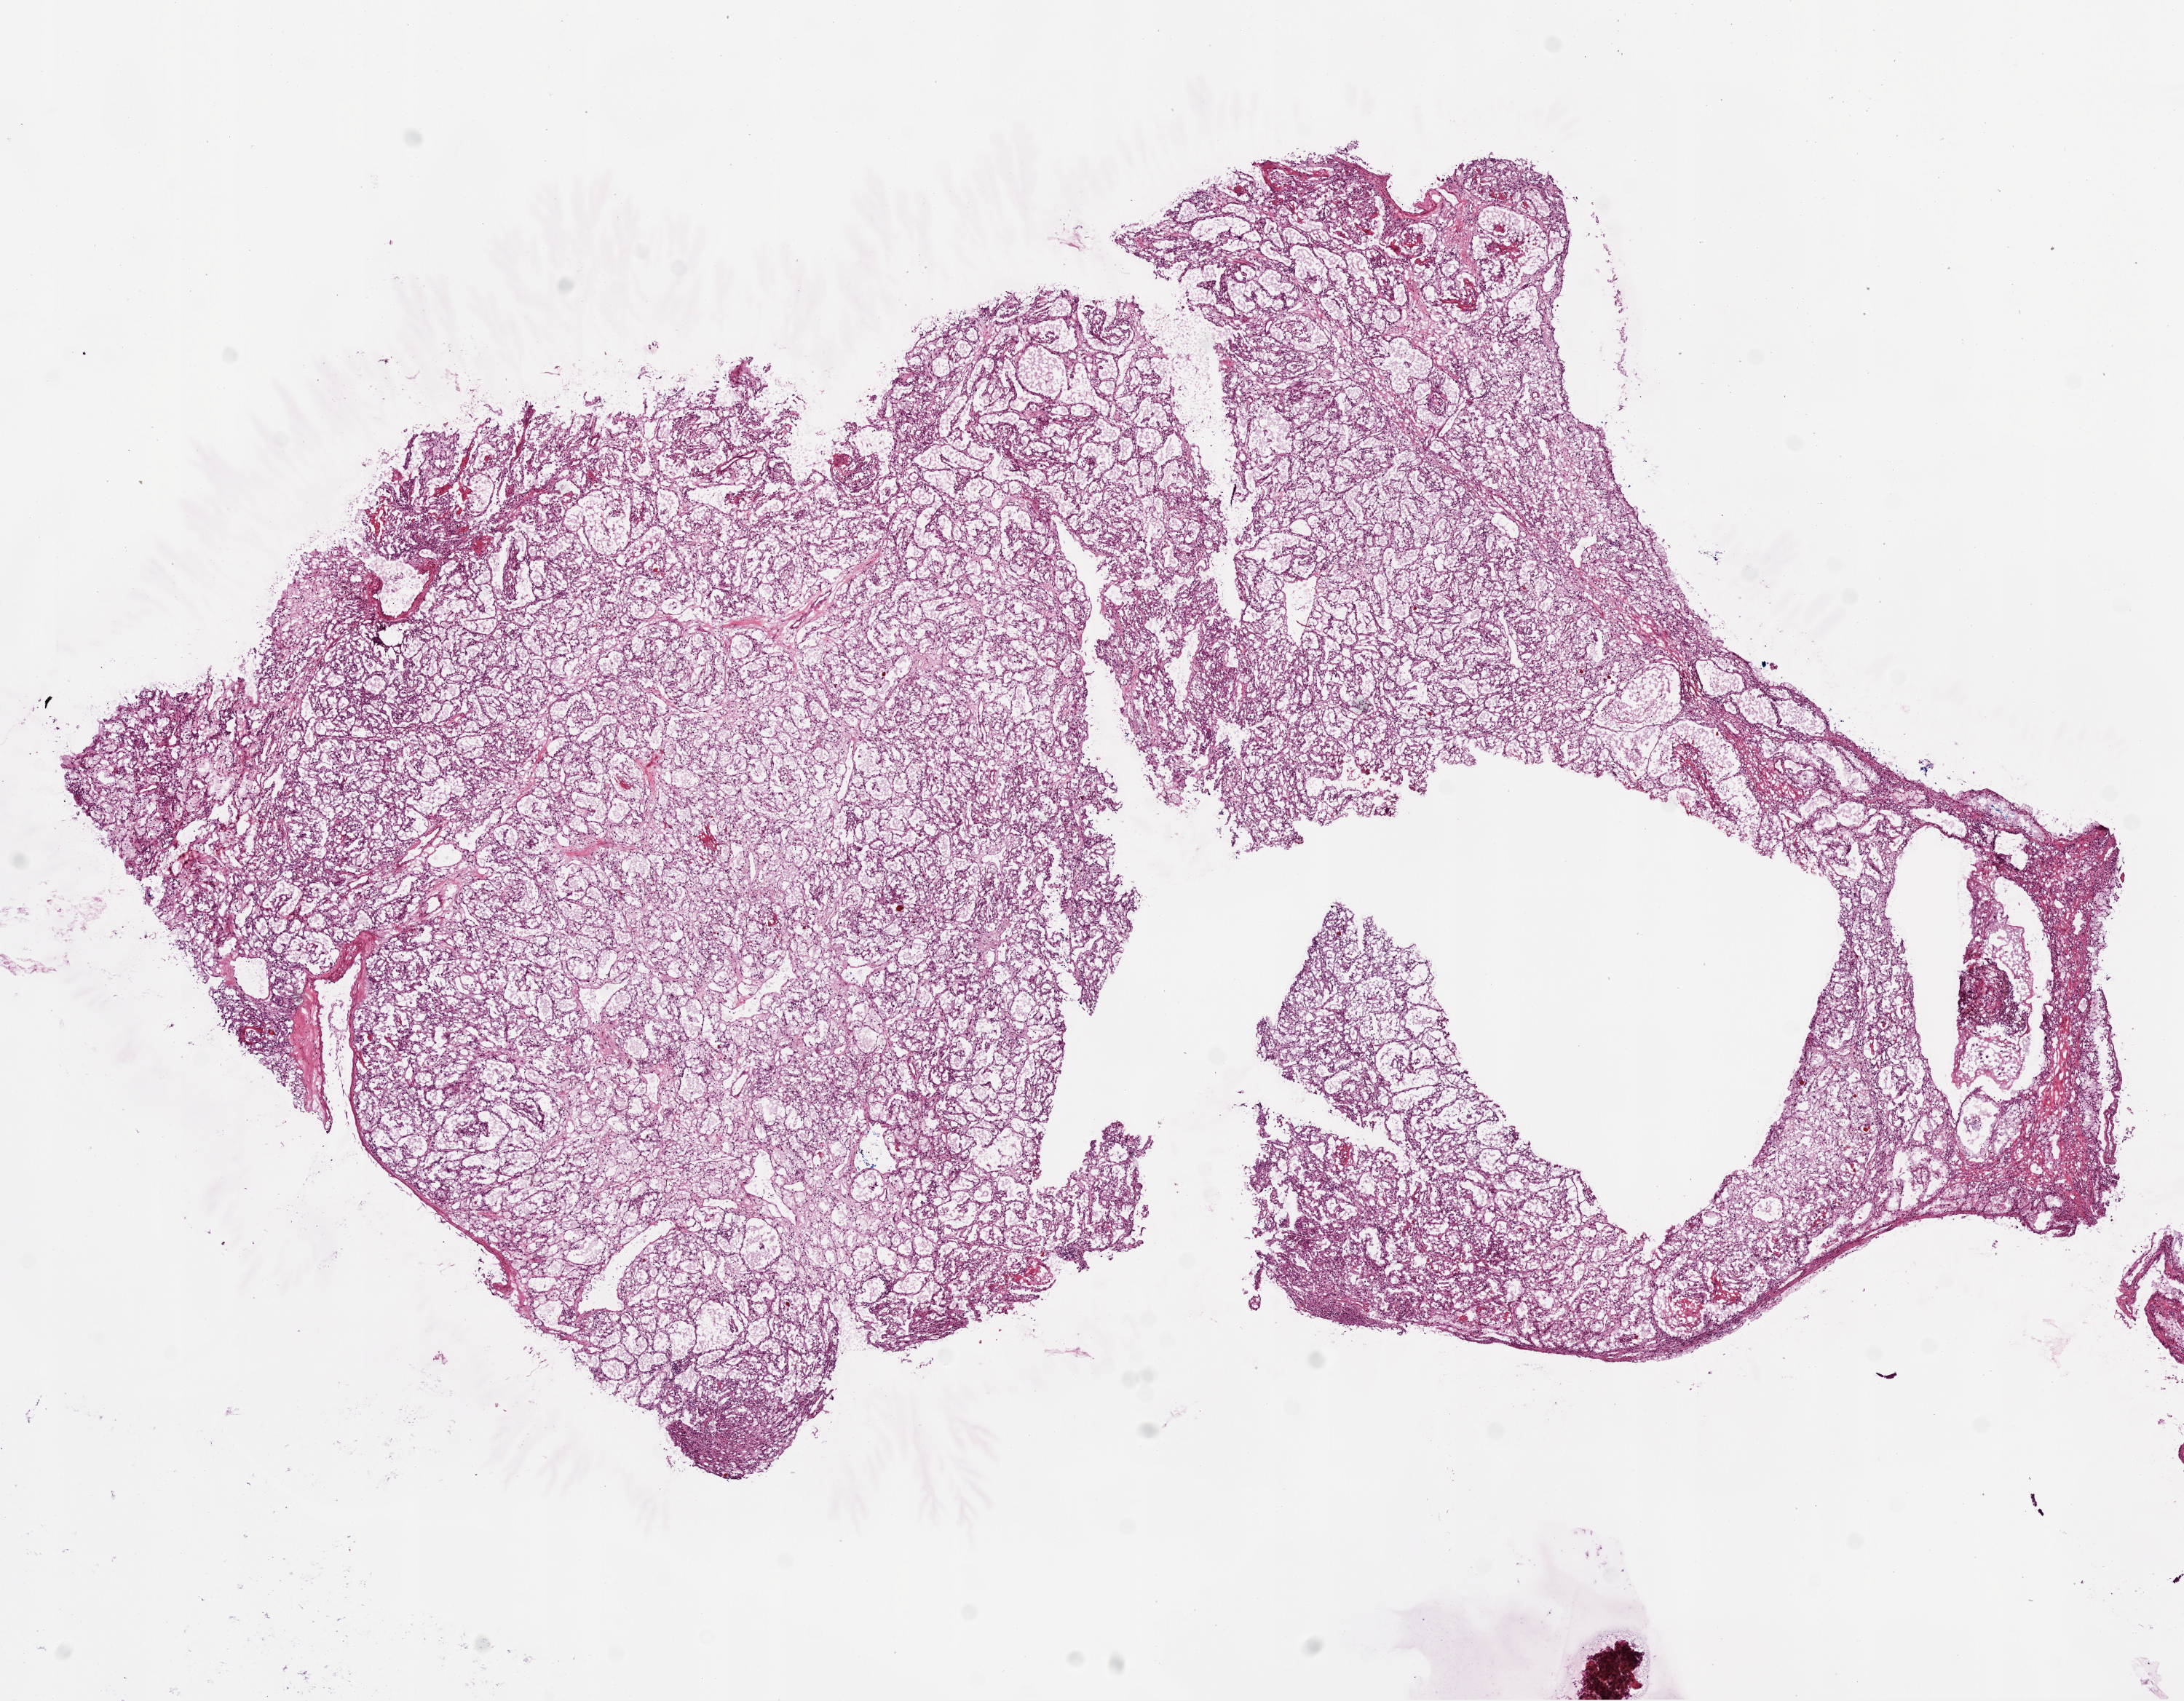
Whole-slide histology image, H&E-stained — a low-resolution overview of the entire scanned area, about 12.0 x 9.4 mm (slide scanned at 20x). Frozen section. Kidney, primary tumour sample. Patient: female, age at initial diagnosis 55 years. Histologic grade: G2 (moderately differentiated). Composition of this section per pathologist review: tumour cells 94%, tumour nuclei 95%, normal cells 0%, stromal cells 5%, necrosis 1%.
• AJCC pathologic stage: I
• diagnosis: Clear cell adenocarcinoma, NOS